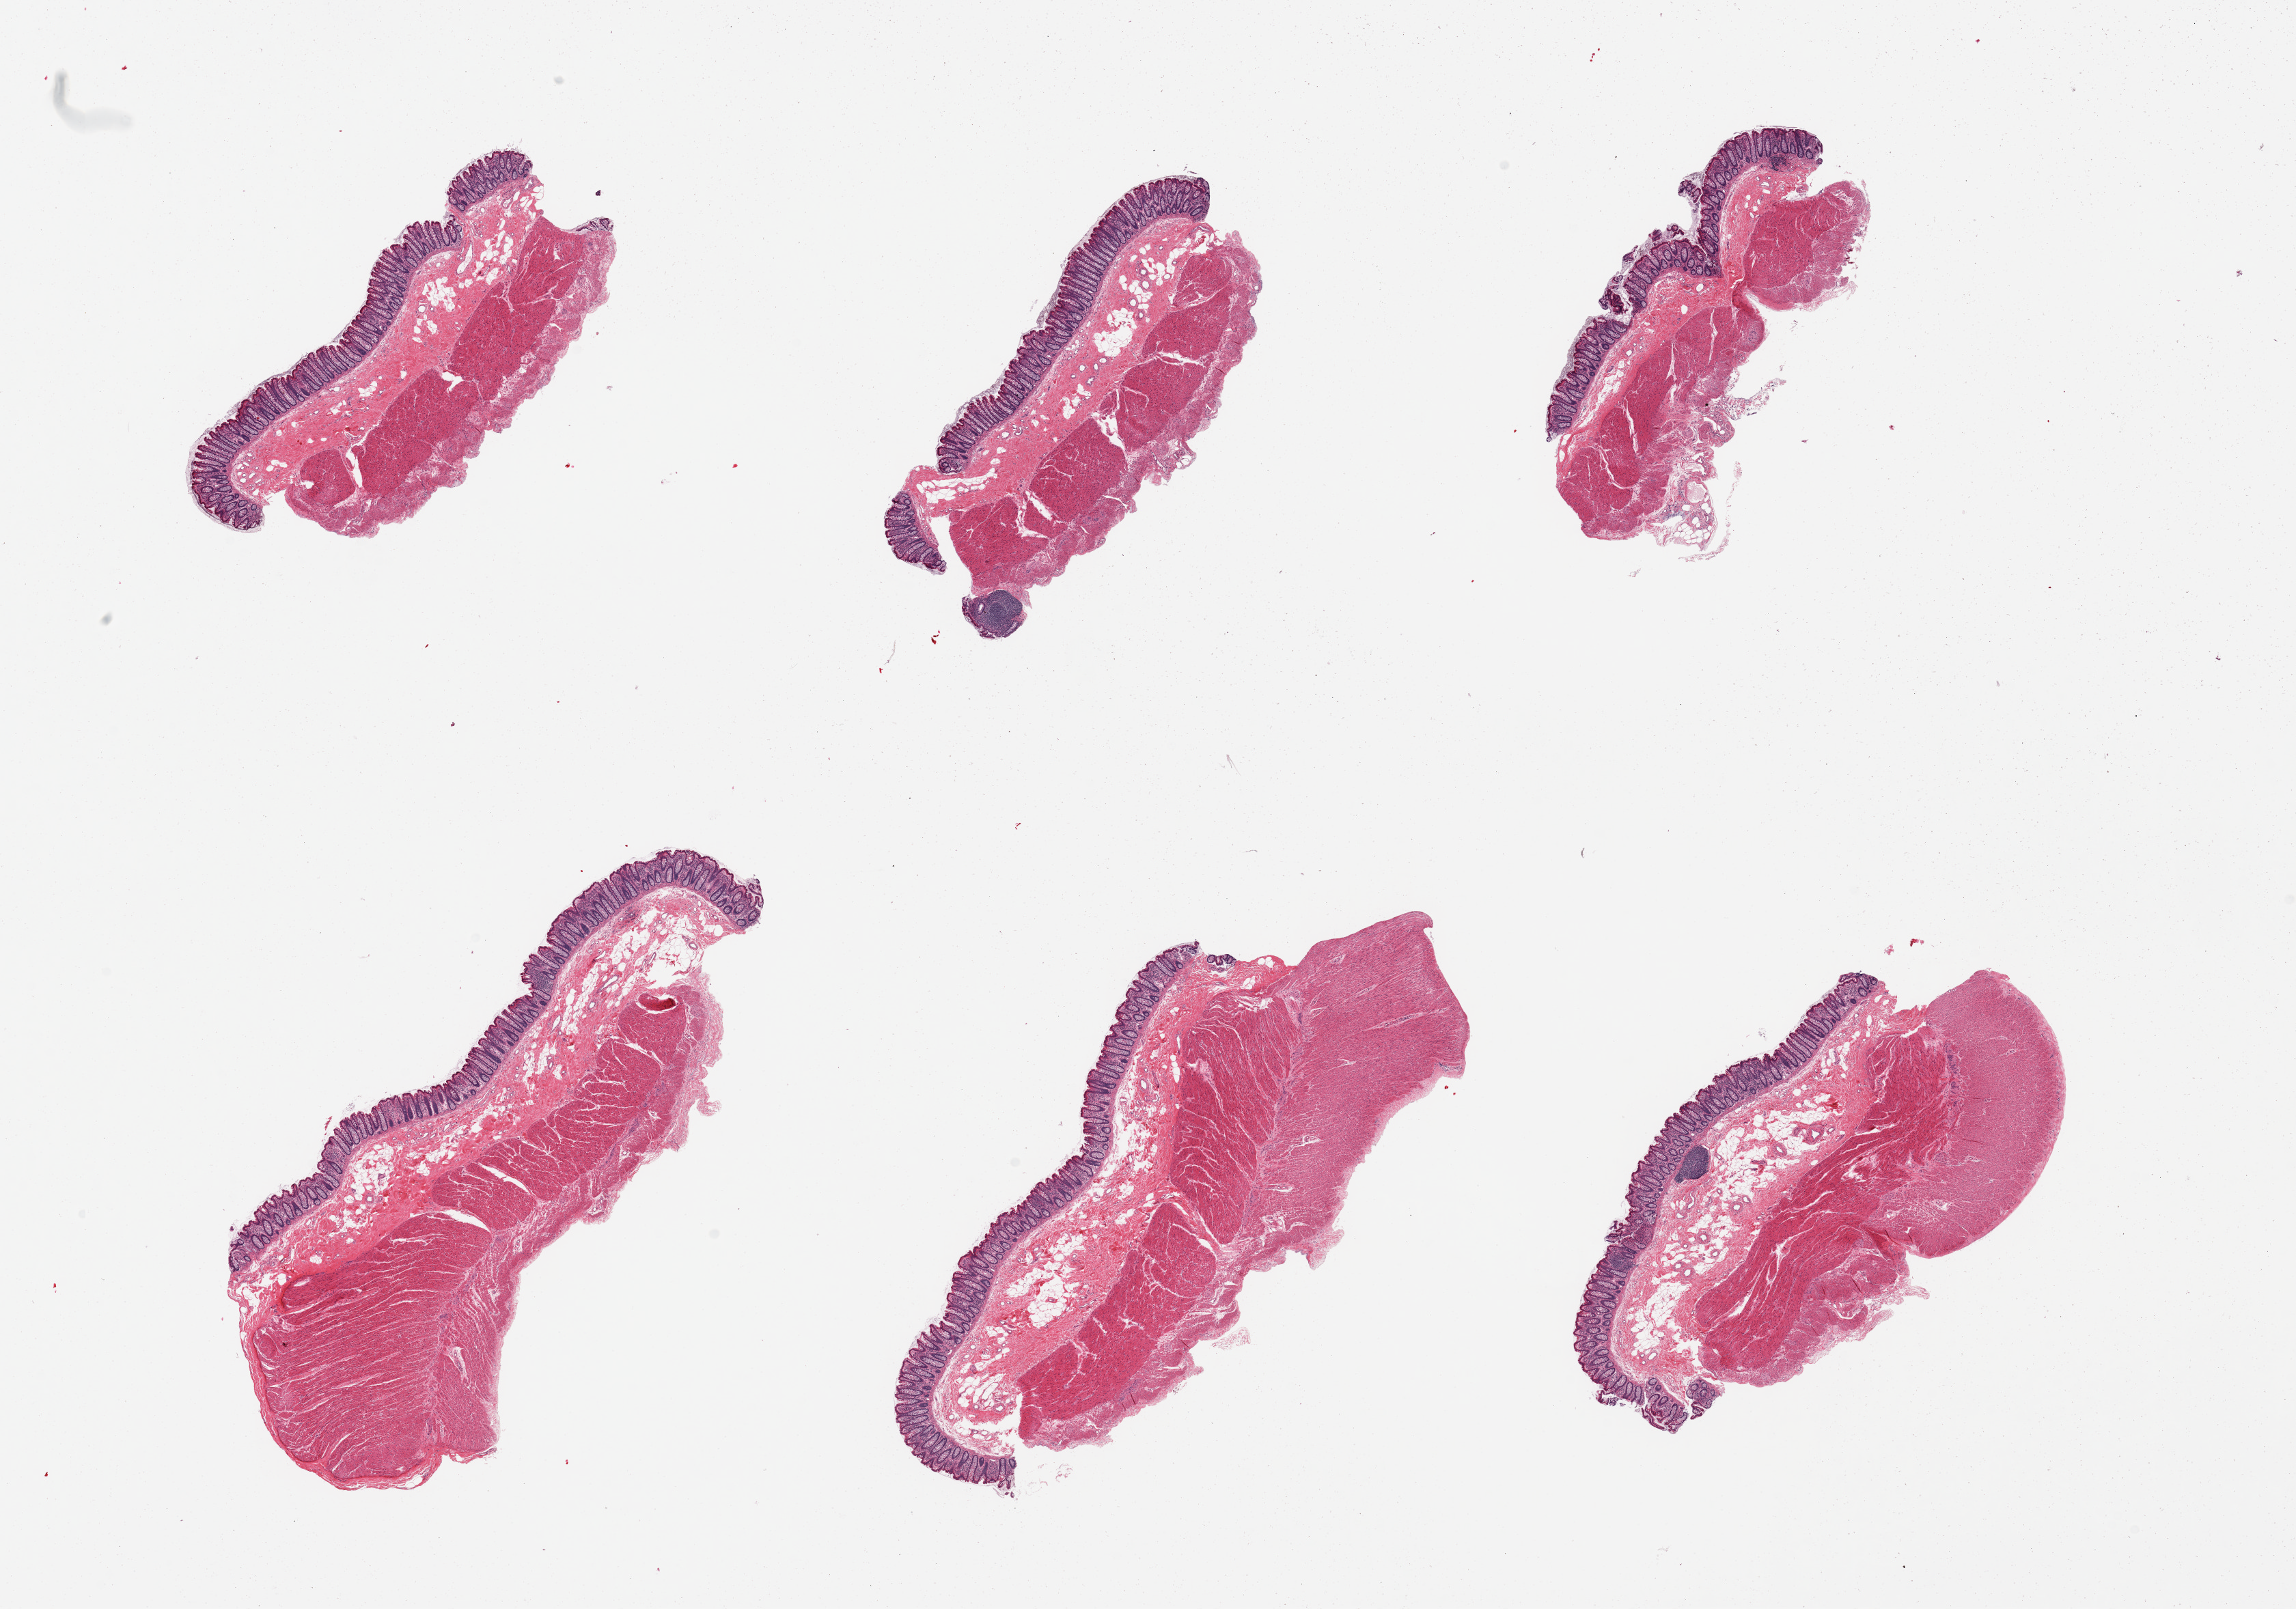
H&E whole-slide image — whole scanned area (about 26.6 x 18.6 mm) shown as a low-resolution overview, PAXgene-fixed paraffin-embedded (PFPE) section, sampled site (target tissue): transverse colon, tissue donor sample. Donor sex: female.
Reviewer comment on this tissue sample: 6 pieces, mucosa is generally well-preserved, ~10%-15% thickness.